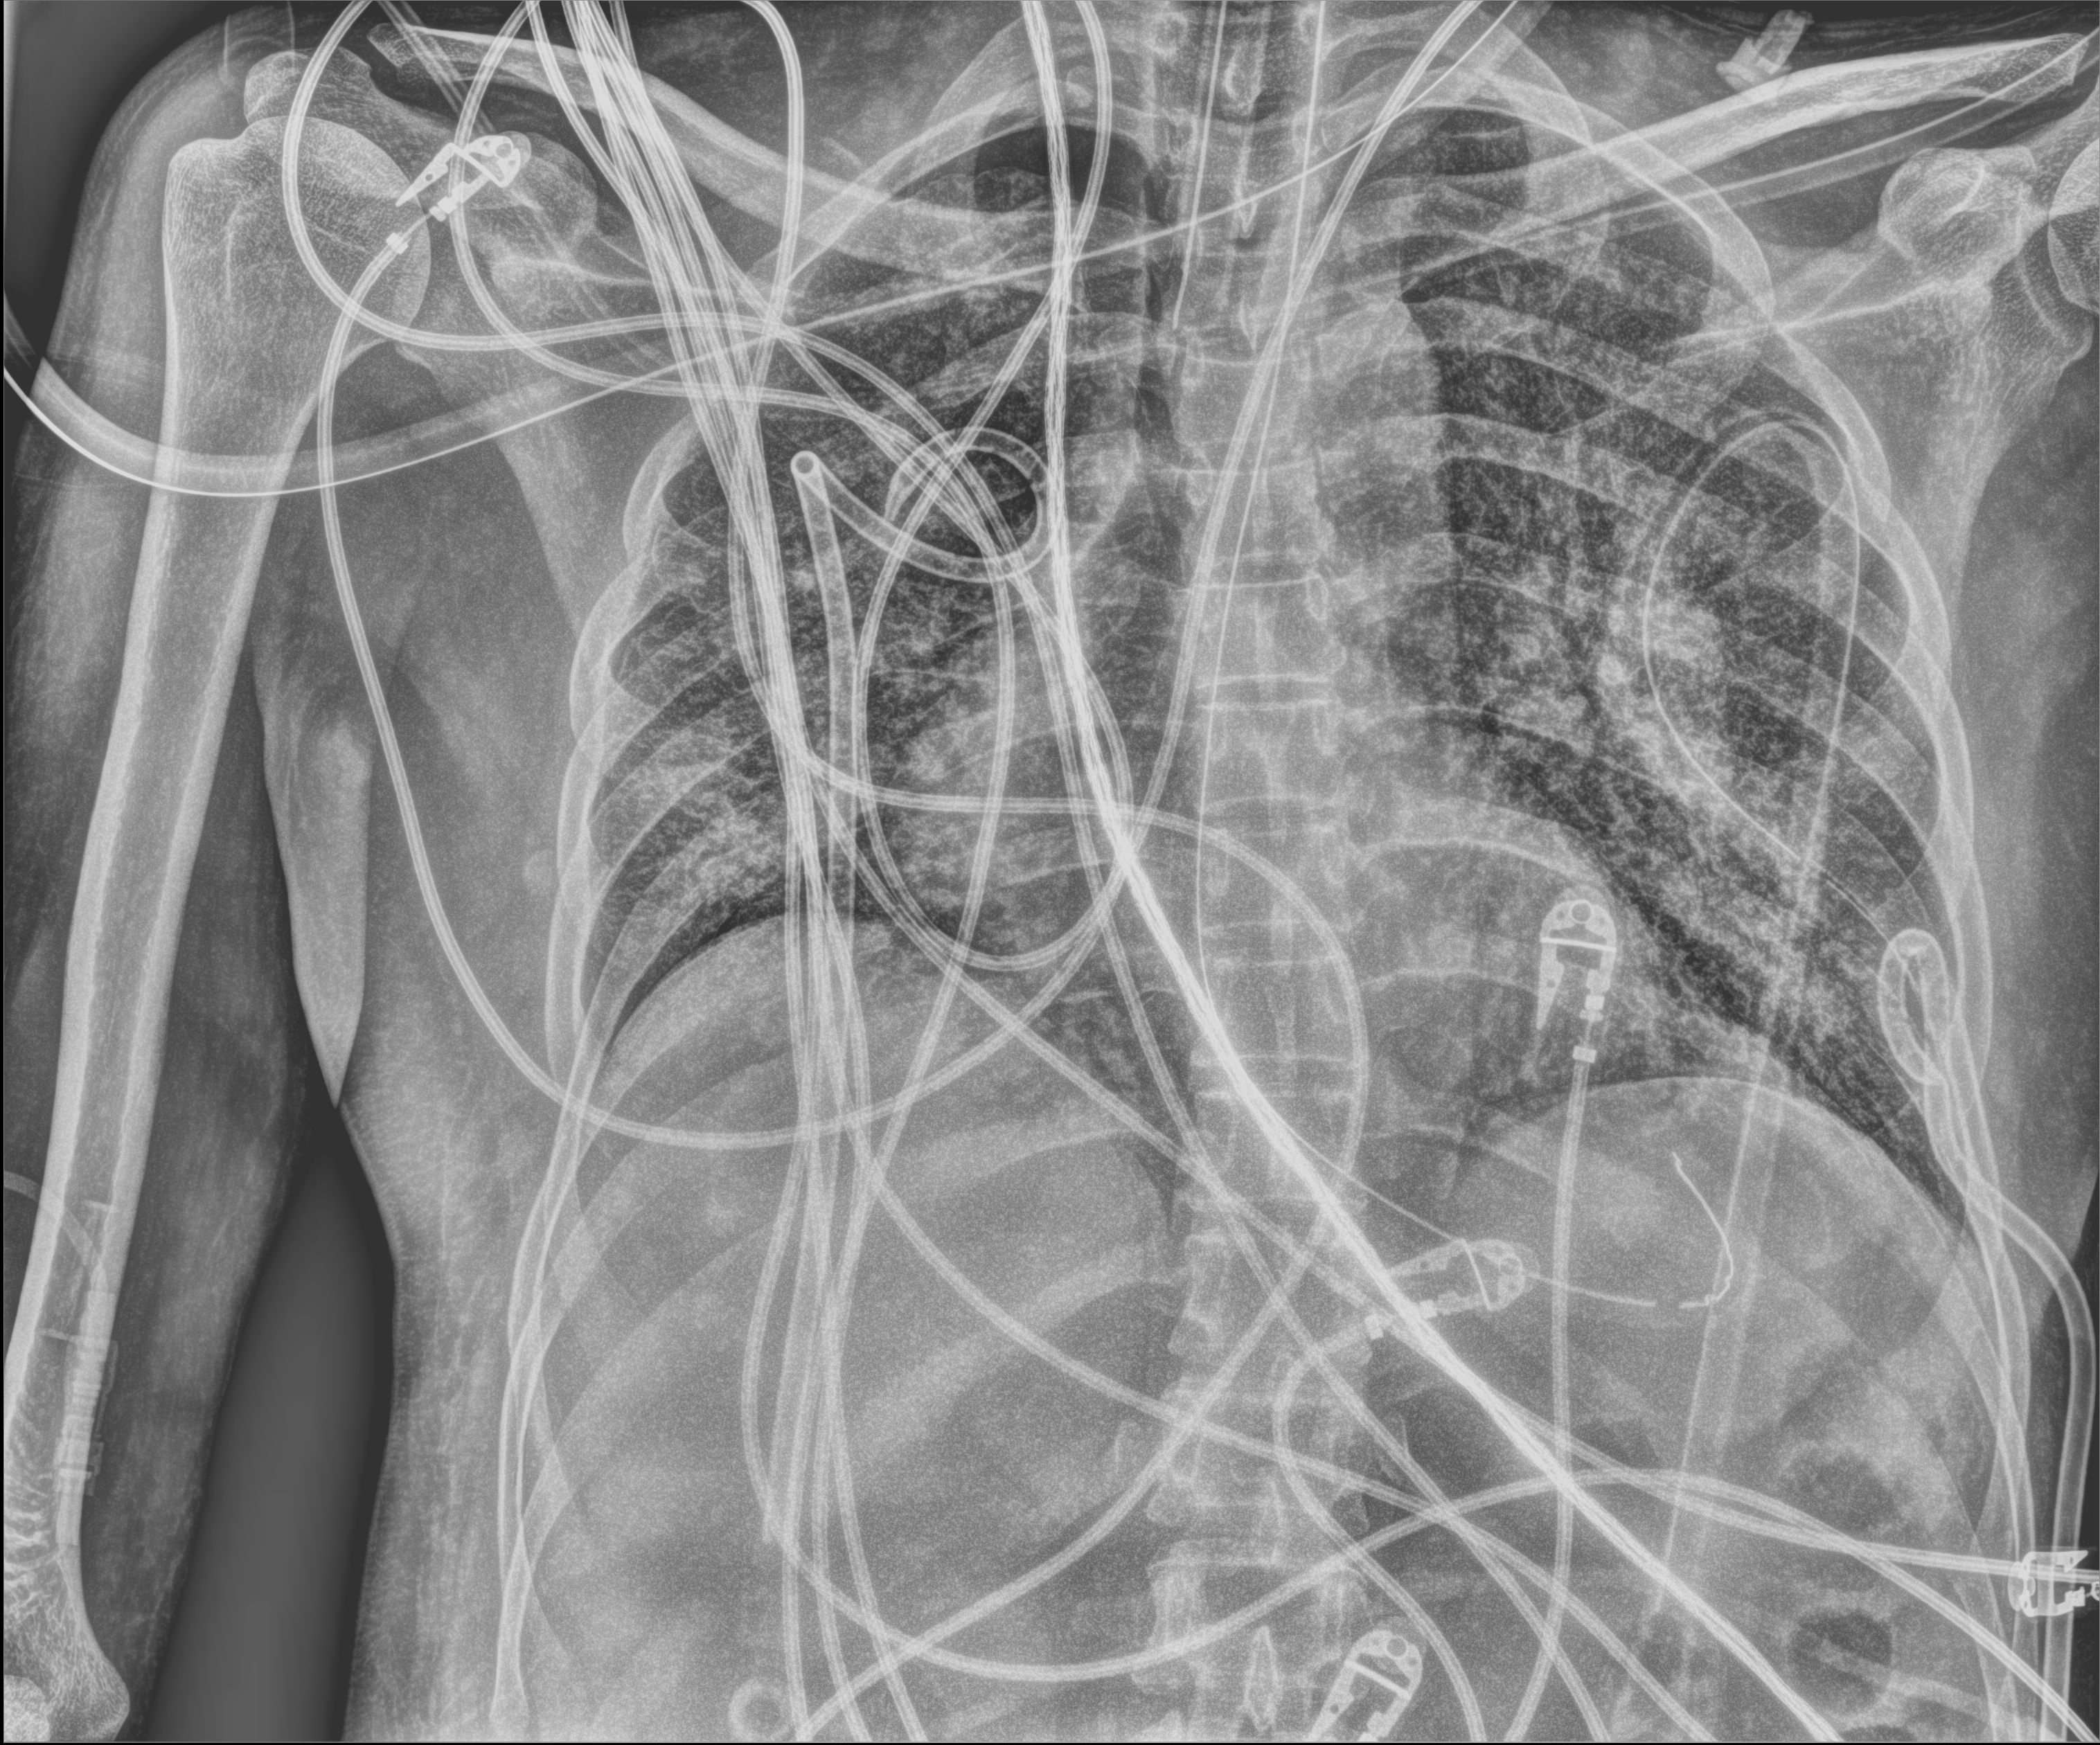
Portable chest radiograph, anteroposterior (AP) projection. Adult patient hospitalised with COVID-19, age 18–59 years.
From the hospital-stay record, not from the radiograph (when in the stay this image was taken is not recorded): smoking status (admission record): never; mechanically ventilated during this hospital stay: yes; admitted to intensive care during this hospital stay: yes.